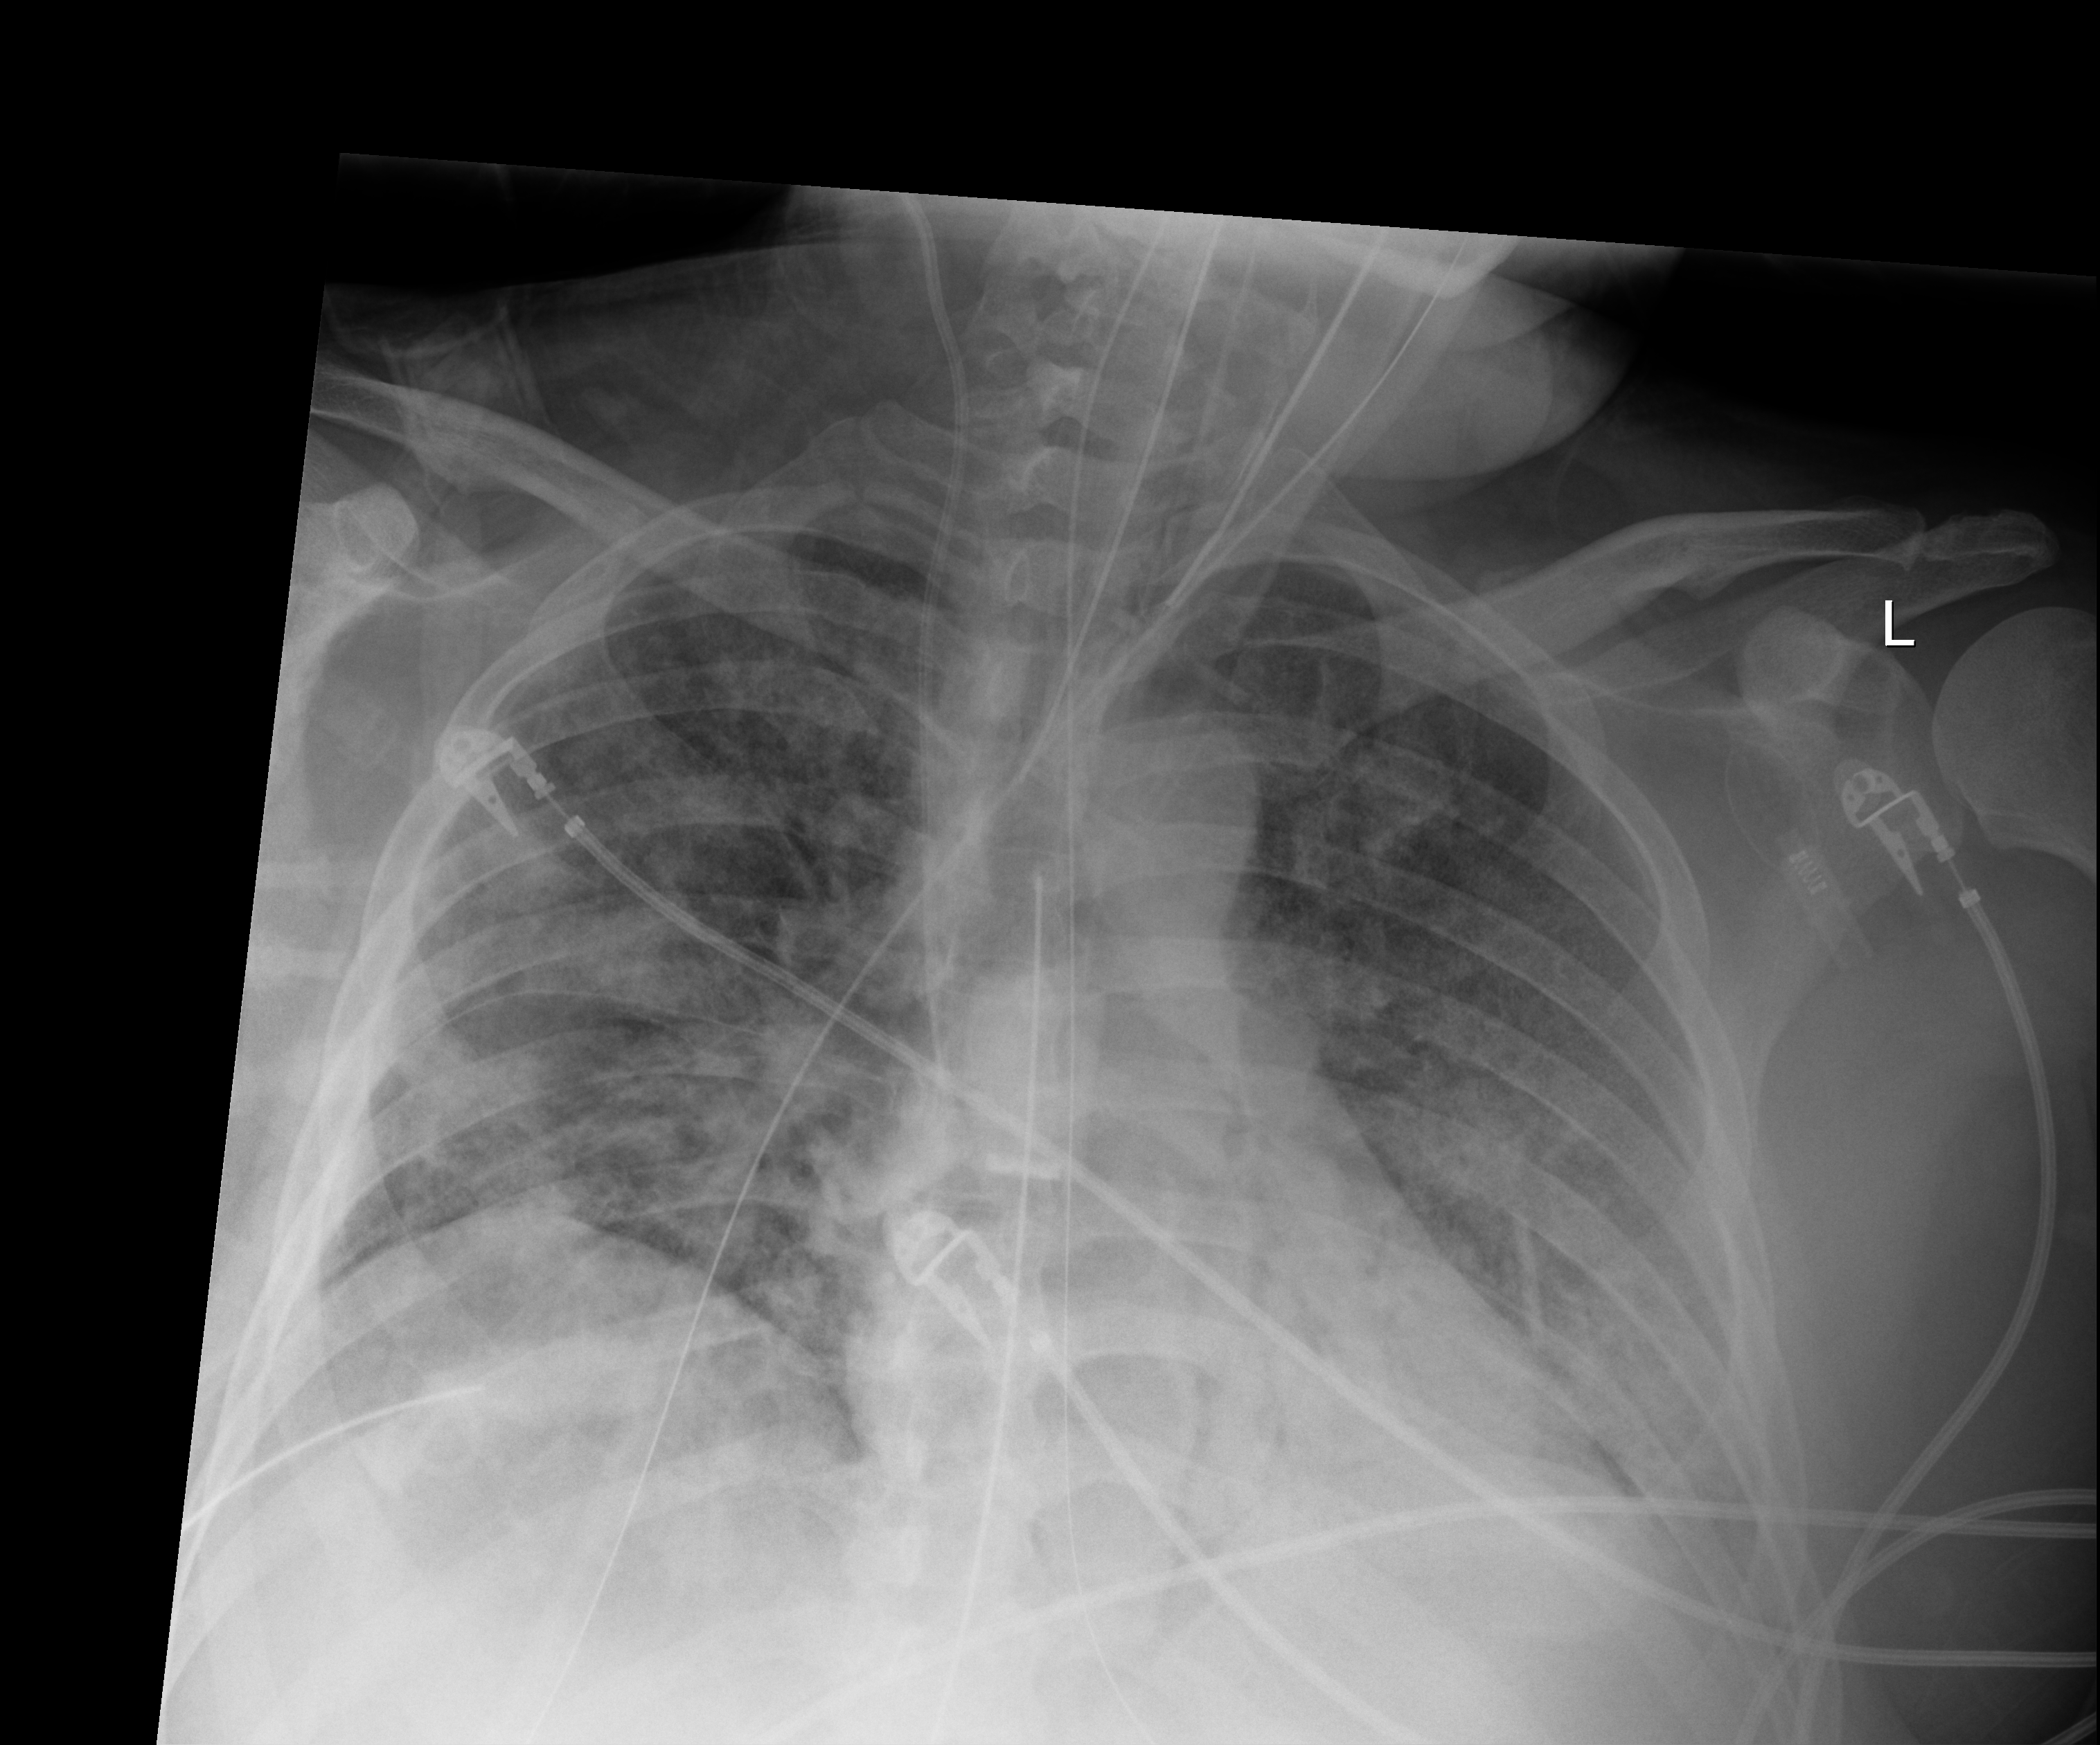
Bedside chest radiograph (digital radiography). Male patient hospitalised with COVID-19, age 18–59 years.
Hospital-stay facts (about this admission, not read from this image; timing relative to this image not recorded): admitted to intensive care during this hospital stay: yes; mechanically ventilated during this hospital stay: yes; COPD (admission record): no.